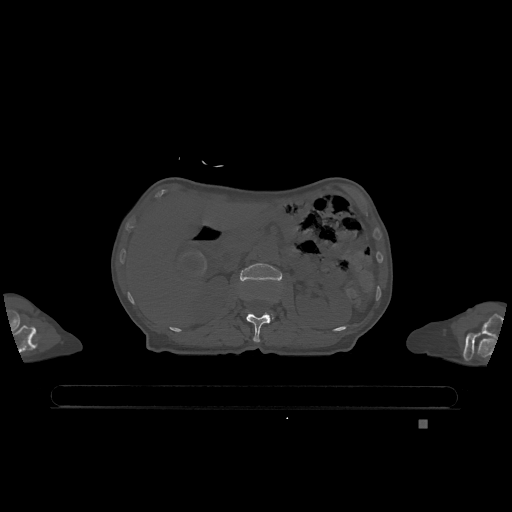
CT including the spine, one axial slice; position 455 of 1317 along the scan axis; bone window (W 1800 / L 400 HU); 512 × 512 image matrix. Patient: female, 74 years. Case-level facts recorded for this patient, not image findings: primary cancer: lung; vertebrae with lytic lesions (as recorded): T1, T4, T5, T6, L4, L5.
Outlined on this slice (semi-automatically segmented with operator editing):
- L1 vertebra: bounding box [x1, y1, x2, y2] px = [246, 313, 271, 343]
- L2 vertebra: [240, 263, 282, 281]